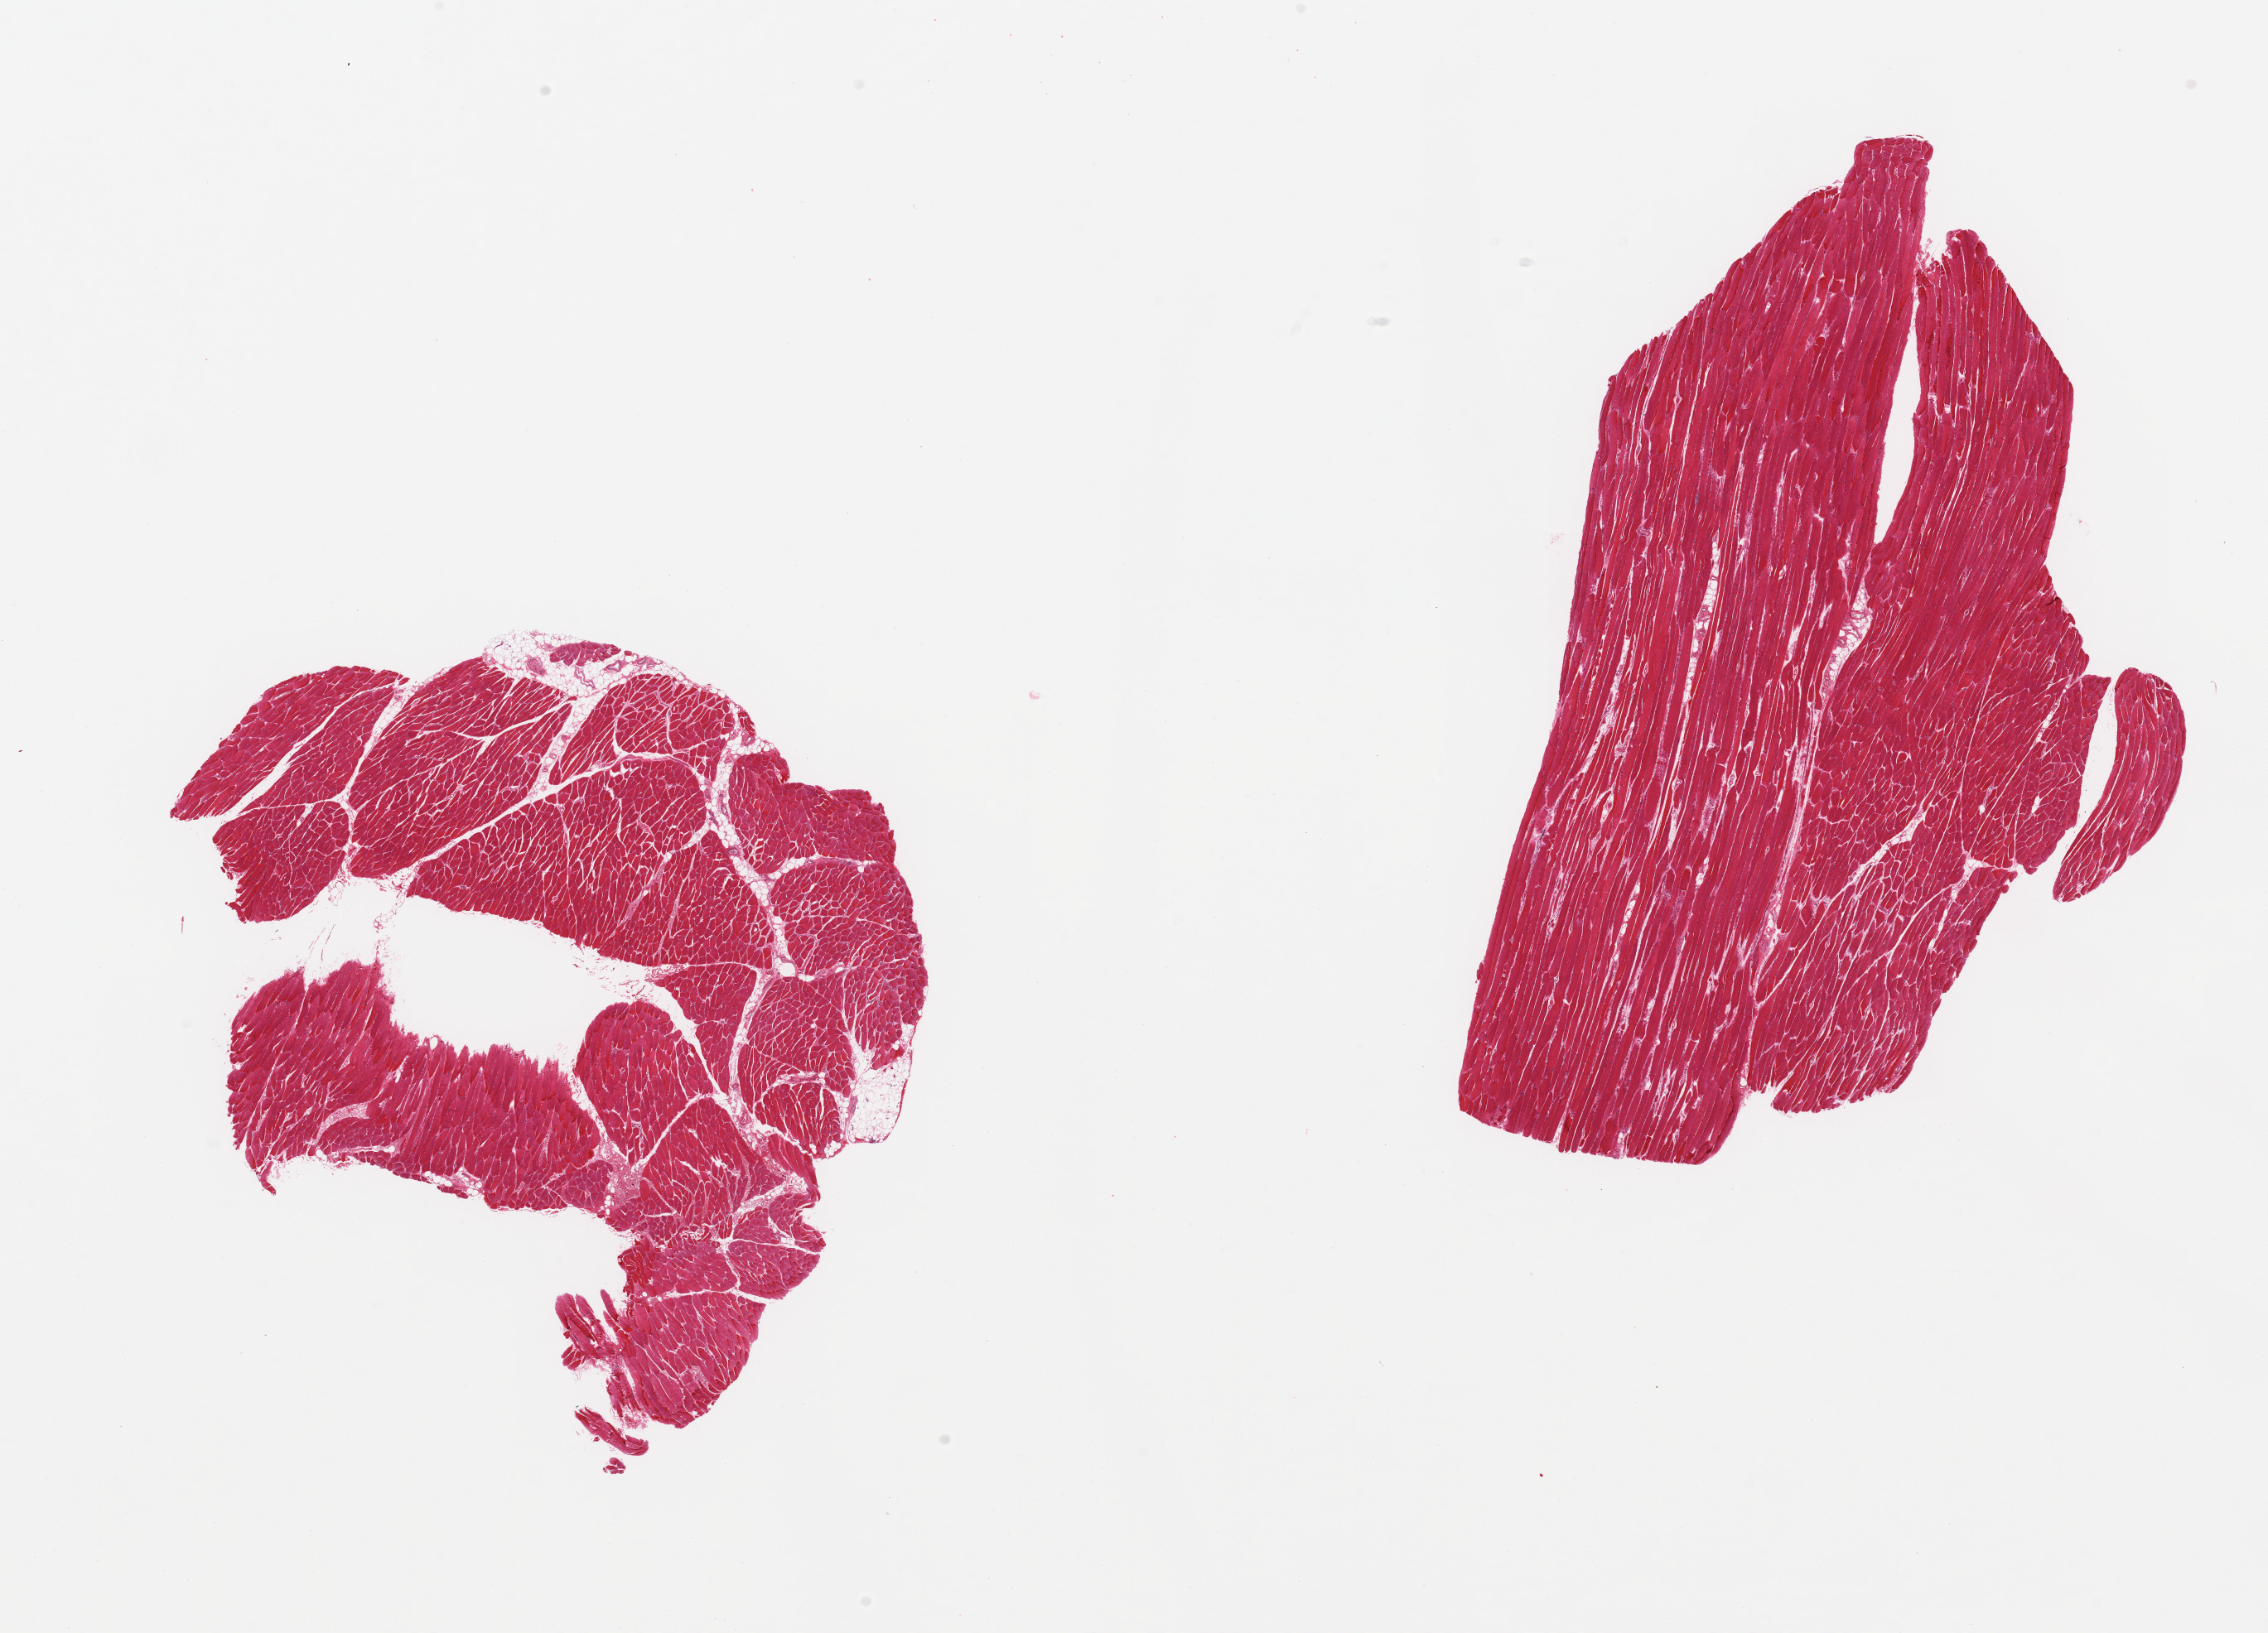
Digitized hematoxylin and eosin (H&E)-stained section — low-resolution overview of the scanned area, about 21.7 x 15.6 mm (from a 20x scan); PAXgene-fixed, paraffin-embedded tissue; section of skeletal muscle (target tissue); donor tissue sample.
Reviewer comment on this tissue sample: 2 pieces; <5% fat content.